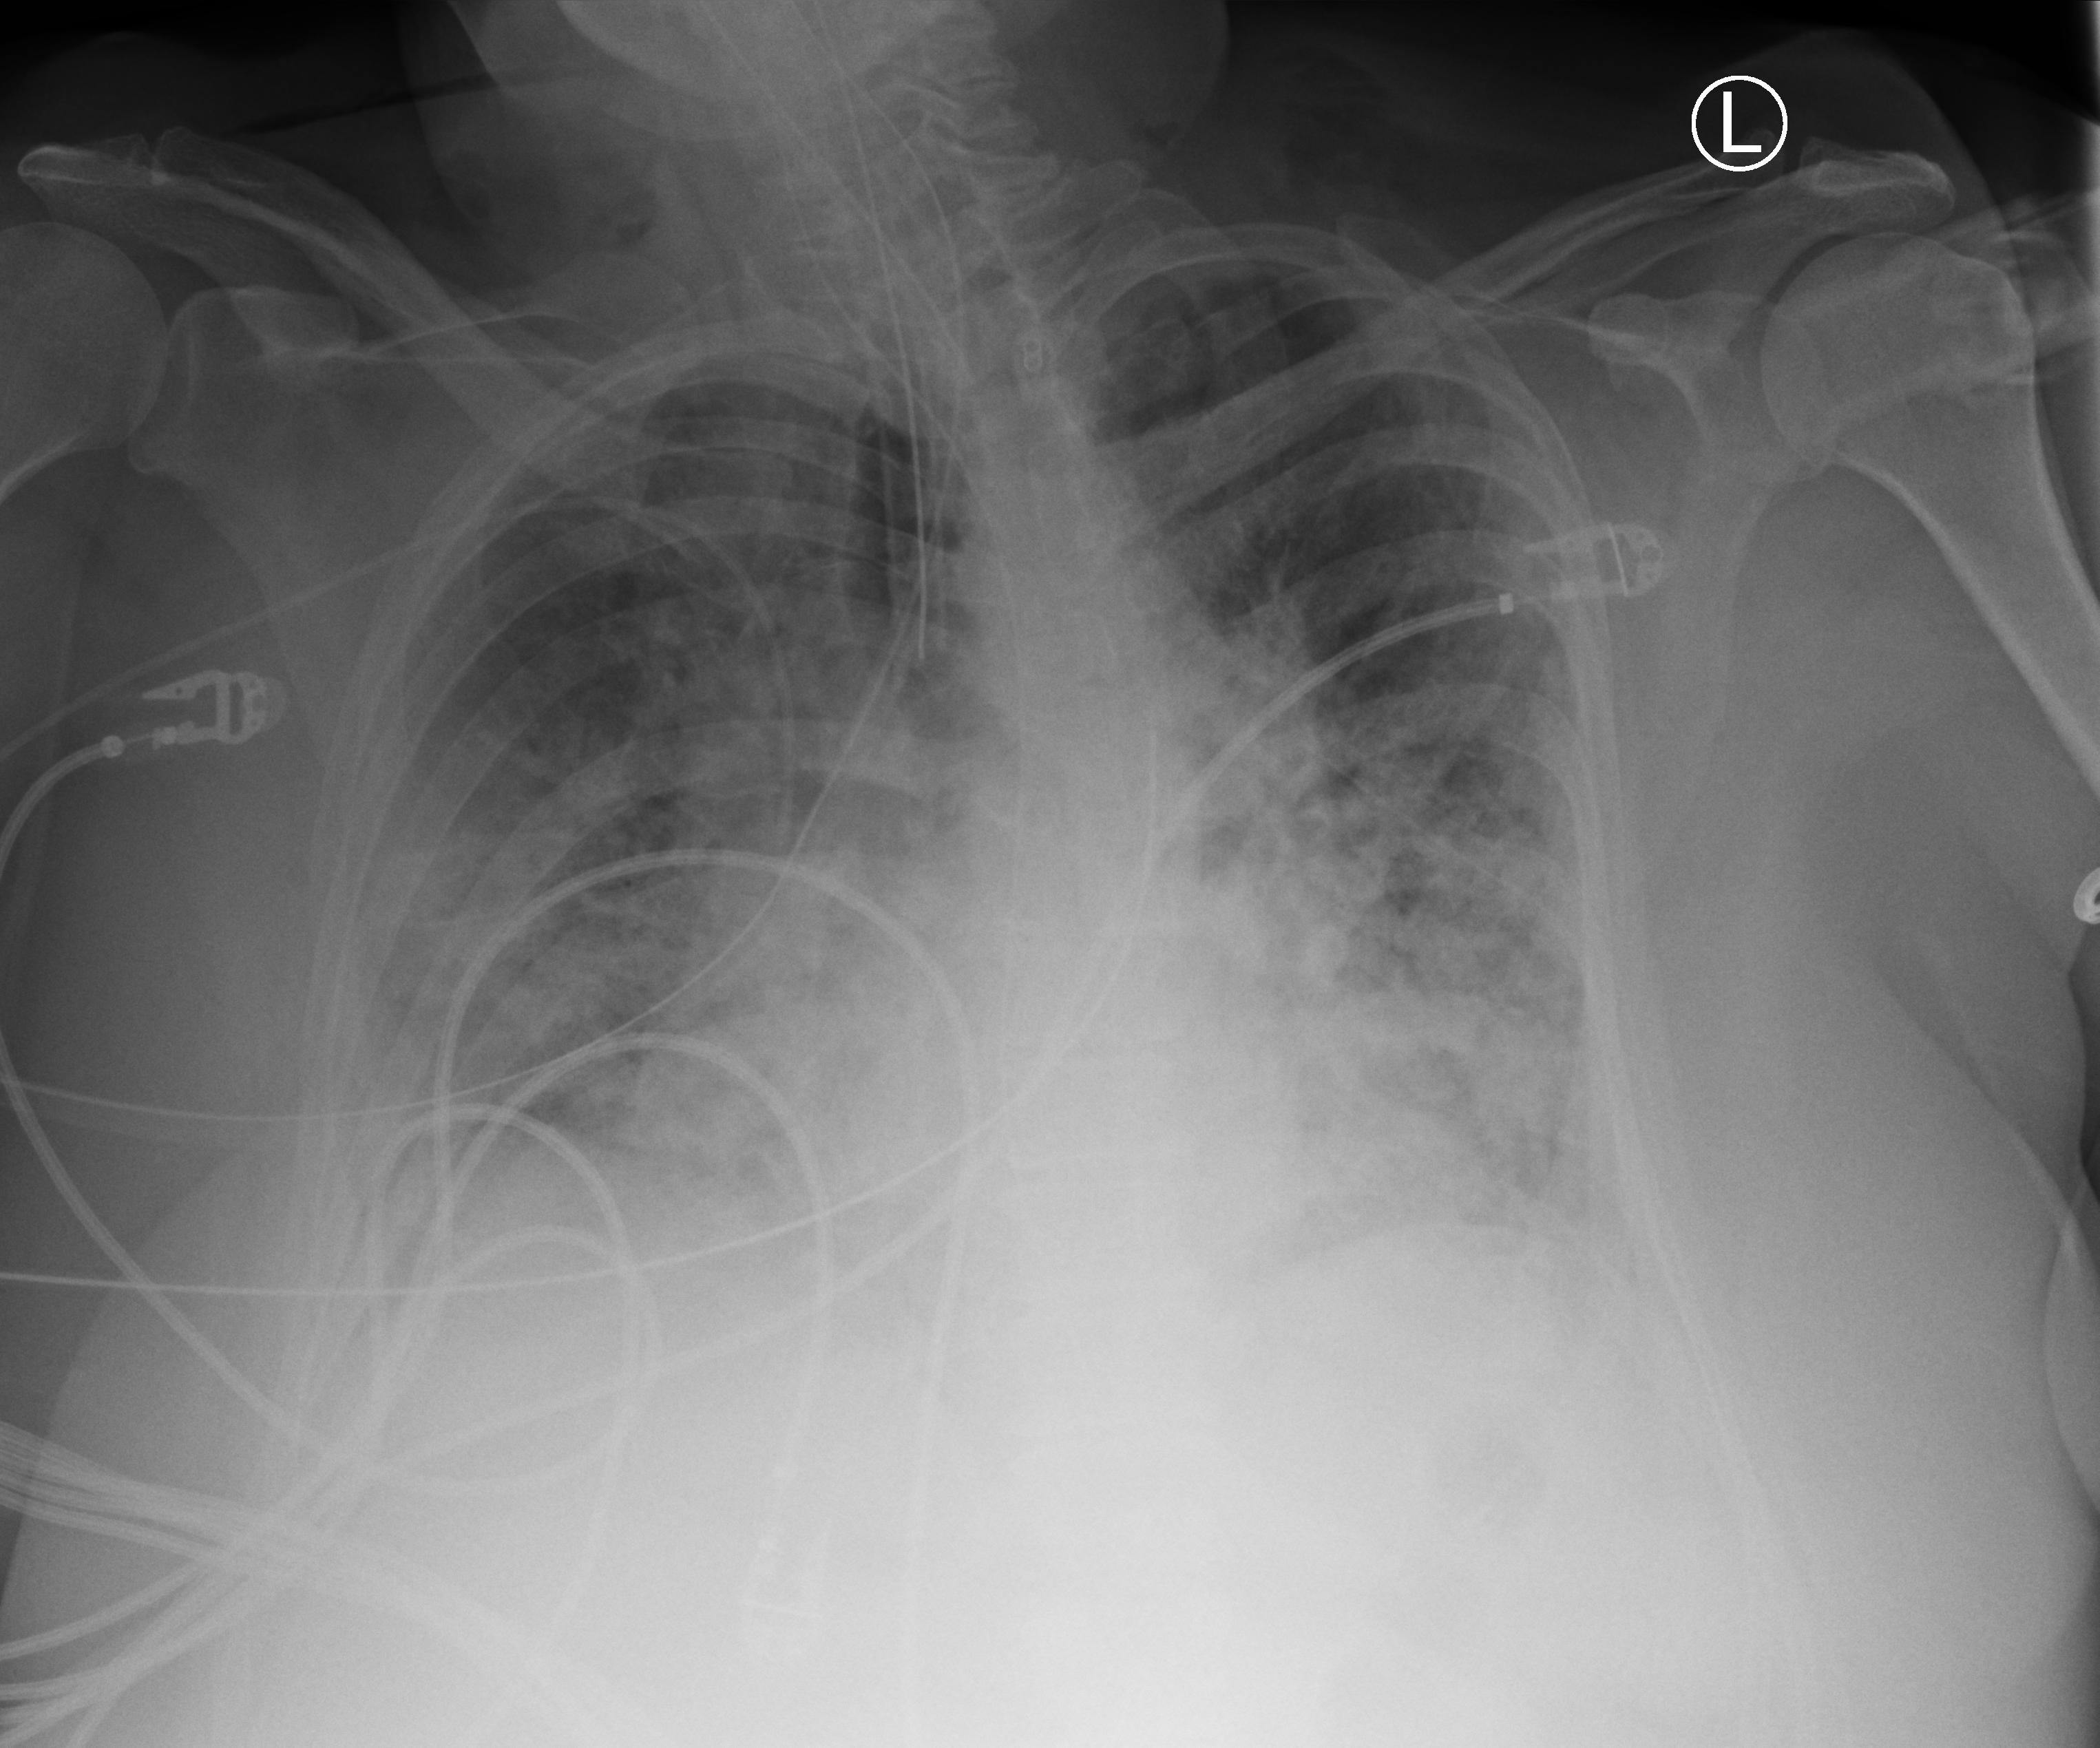
Portable chest radiograph. Female patient hospitalised with COVID-19, age 60–74 years.
Hospital-stay facts (about this admission, not read from this image; timing relative to this image not recorded): admitted to intensive care during this hospital stay: yes; mechanically ventilated during this hospital stay: yes; length of hospital stay: 45 days.